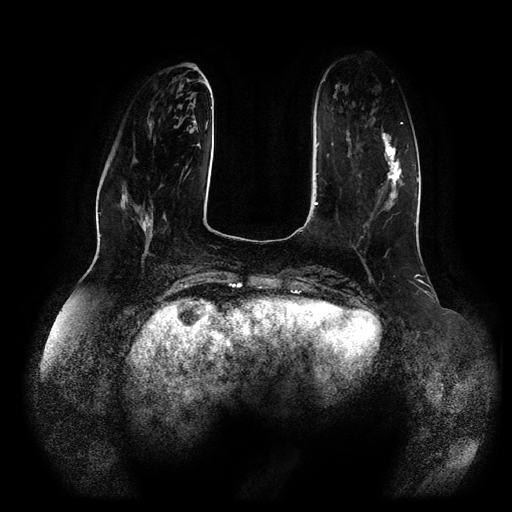
Breast MRI (dynamic contrast-enhanced, multi-phase), one axial slice; position 29 of 116 along the scan axis; dynamic contrast-enhanced series, time point 2 of 5 at this slice position (early post-contrast); 1.5 T; TE 2.5 ms, TR 5.2 ms; 512 × 512 image matrix, field of view 400 × 400 mm. Patient: female, 66 years.
Annotated regions visible in this slice (semi-automatic segmentation, software-assisted and operator-edited):
- breast lesion (labelled 'tumour' in the annotation; benign lesions carry a separate 'benign' label): bounding box <381,133,404,220> (left, top, right, bottom; pixels)